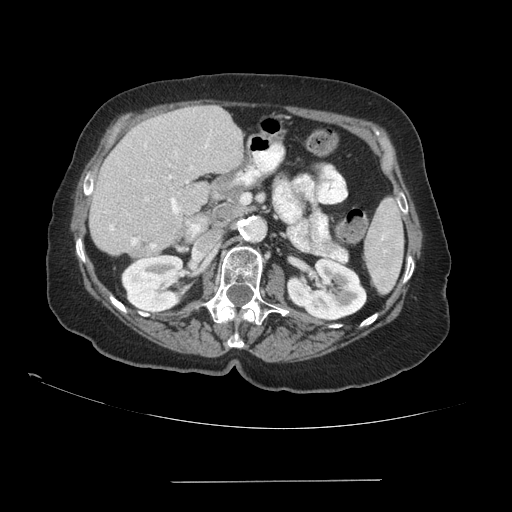
Contrast-enhanced abdominal CT (liver protocol), one axial slice; slice 44 of 89 in the series (ordered by position); 140 kVp; soft-tissue window (W 400 / L 40 HU); 2.5 mm slice thickness; 512 × 512 image matrix. From the clinical record (not read from this slice): diagnosis: hepatocellular carcinoma (patient treated with transarterial chemoembolisation; whether this scan precedes or follows treatment is not stated here); TNM stage (as recorded): Stage-IVA; Child-Pugh class: A; tumour differentiation: poorly differentiated; tumour nodularity: uninodular.
Outlined on this slice (semi-automatic segmentation, software-assisted and operator-edited):
- liver parenchyma outside the tumour (the mass and vessels are separate outlines, so this box may not span the whole liver): bounding box [x1, y1, x2, y2] px = [90, 106, 242, 254]
- liver vessels: [110, 144, 208, 249]